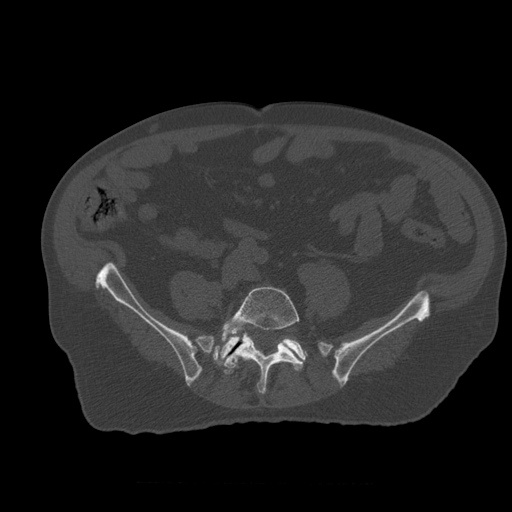
CT including the spine, one axial slice. Slice 139 of 399 in the series (ordered by position). 120 kVp. Bone window (W 1800 / L 400 HU). 512 × 512 image matrix. Patient age 73 years. Case-level facts recorded for this patient, not image findings: primary cancer: prostate.
Annotated regions visible in this slice (semi-automatically segmented with operator editing):
- L4 vertebra: bounding box [x1, y1, x2, y2] px = [244, 357, 246, 360]
- L5 vertebra: [212, 287, 303, 394]